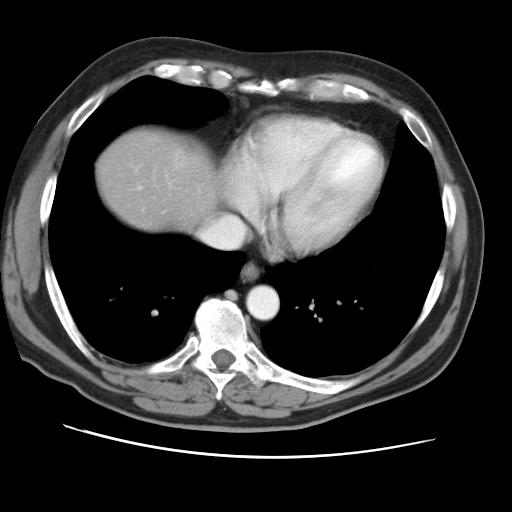
Contrast-enhanced abdominal CT, one axial slice; slice 46 of 49 in the series (ordered by position); intravenous contrast given; soft-tissue window (W 400 / L 40 HU); 5 mm slice thickness; 512 × 512 image matrix, field of view 374 × 374 mm. Male patient, age 59 years. From the clinical record (not read from this slice): diagnosis: colorectal cancer liver metastases, imaged before liver resection; multiple liver metastases: yes; largest metastasis: 6.3 cm.
Annotated regions visible in this slice (manually delineated by an expert):
- liver: bounding box [x1, y1, x2, y2] px = [100, 134, 216, 230]
- planned liver remnant (the part of the liver to remain after resection): [100, 134, 216, 230]
- liver metastasis: [174, 150, 187, 168]